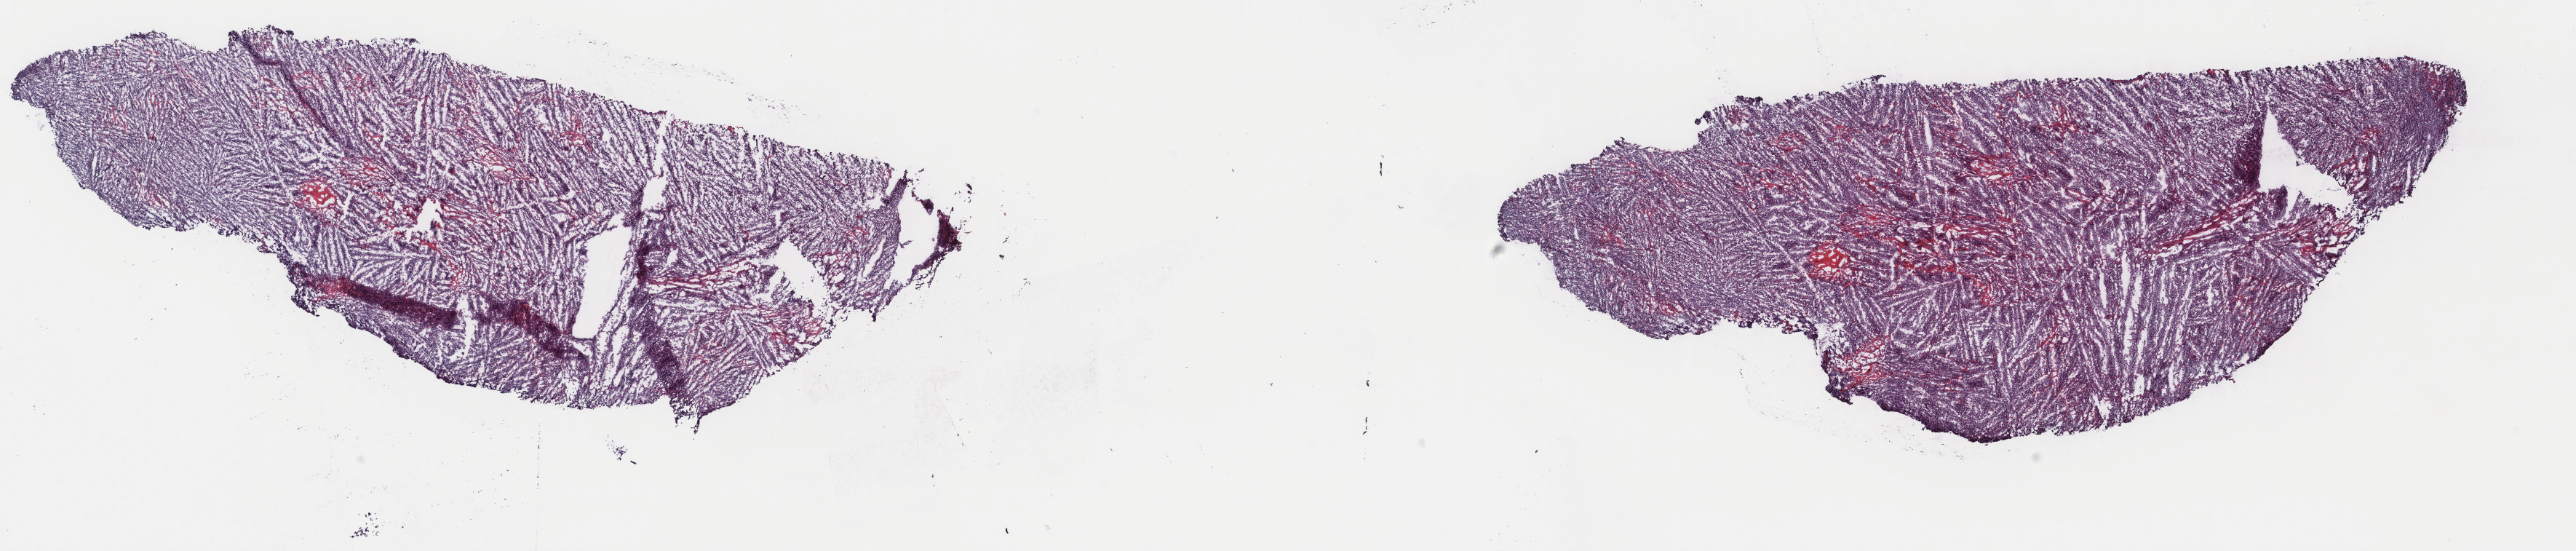
Digitized H&E tissue section (whole slide) — a low-resolution overview of the entire scanned area, about 28.1 x 6.0 mm; frozen section from the top of the tissue portion; primary tumour sample from the lymphoid tissue. Male patient; age at initial diagnosis 67 years. Pathologist review of this section (percent, as recorded): tumour cells 95%, tumour nuclei 95%, normal cells 3%, stromal cells 2%, necrosis 0%. Inflammatory infiltration, as recorded: lymphocyte infiltration 3%, monocyte infiltration 2%, neutrophil infiltration 0%.
- histologic diagnosis: Diffuse large B-cell lymphoma, NOS (lymph nodes of axilla or arm)